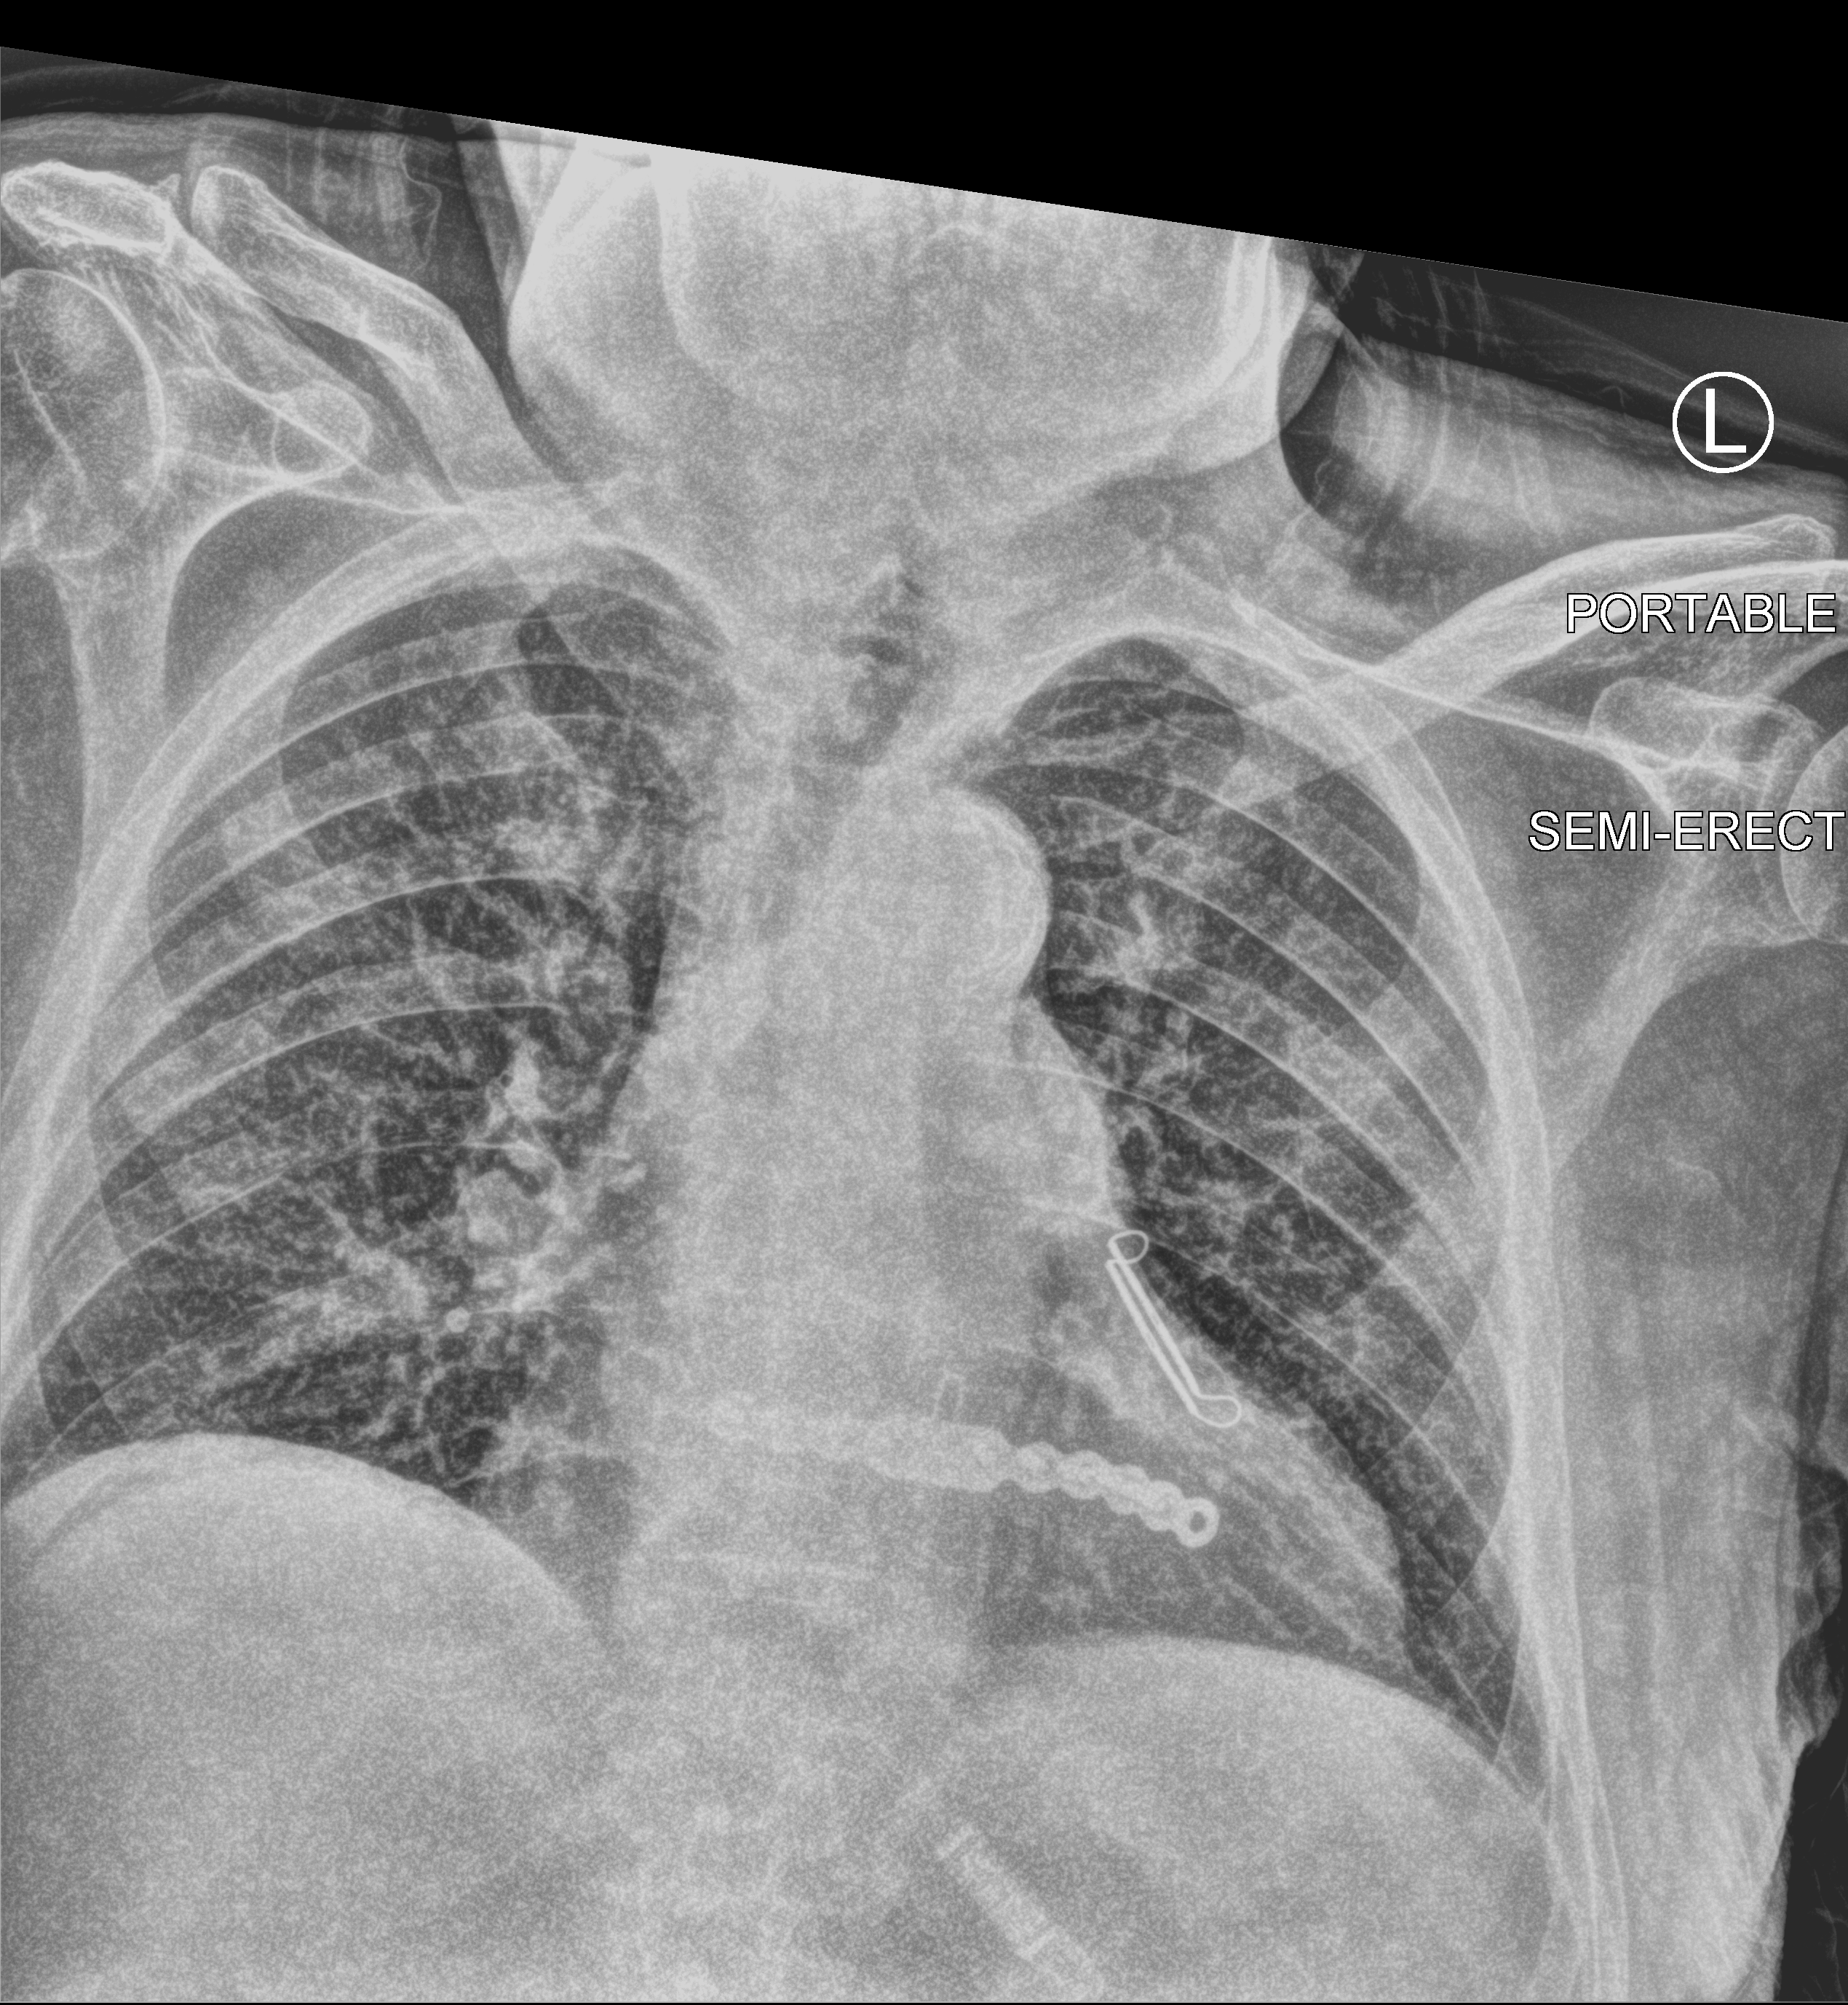
Chest X-ray (portable); anteroposterior (AP) projection. Male patient hospitalised with COVID-19, age 75–90 years.
Hospital-stay facts (about this admission, not read from this image; timing relative to this image not recorded): chronic kidney disease (admission record): no.